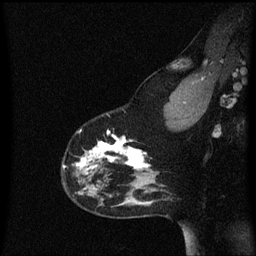
Breast MRI (dynamic contrast-enhanced), one sagittal slice; dynamic contrast-enhanced series, image 2 of 3 at this slice position (ordered by acquisition); 1.5 T; TE 4.2 ms, TR 8.4 ms; 256 × 256 image matrix, field of view 200 × 200 mm. Female patient, age 33 years.
Annotated regions visible in this slice (semi-automatic segmentation, software-assisted and operator-edited):
- analysis volume of interest (the breast-tissue region the enhancement analysis was run in; not a lesion): box from (x=62, y=114) to (x=152, y=191) px
- tumour enhancement mask (voxels above the 70 % enhancement threshold inside the analysis volume of interest): (x=64, y=130)–(x=151, y=169)